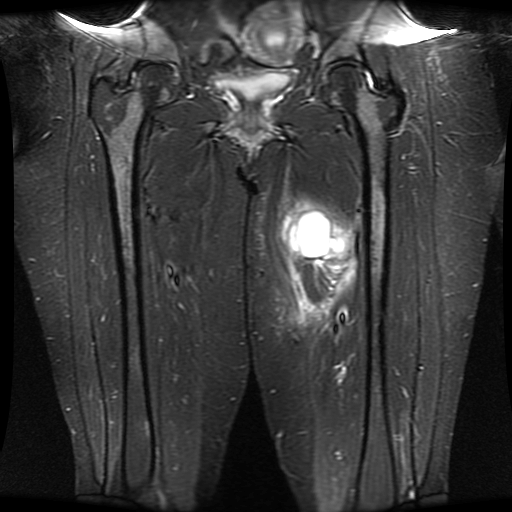
MRI of an extremity soft-tissue mass, one coronal slice. Position 14 of 30 along the scan axis. STIR. 512 × 512 image matrix, field of view 460 × 460 mm. Female patient. Case-level facts recorded for this patient, not image findings: histological type: myxofibrosarcoma; grade: intermediate; site of the primary tumour: left thigh.
Annotated regions visible in this slice (expert manual segmentation):
- gross tumour volume including surrounding oedema: box from (x=278, y=182) to (x=359, y=328) px
- gross tumour volume (mass): (x=288, y=210)–(x=346, y=259)